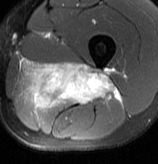
MRI of an extremity soft-tissue mass, one axial slice. Slice 40 of 70 in the series (ordered by position). T2-weighted fat-saturated. MR volume resampled by the dataset authors to the PET/CT grid (not the native acquisition matrix). 3.27 mm slice thickness. 158 × 164 image matrix. Male patient. From the clinical record (not read from this slice): histological type: extraskeletal osteosarcoma; grade: high; site of the primary tumour: left adductur.
Annotated regions visible in this slice (expert contour drawn on MRI and transferred to this co-registered scan by the dataset authors):
- gross tumour volume (mass): bounding box (x1, y1, x2, y2) in pixels: (15, 60, 121, 108)